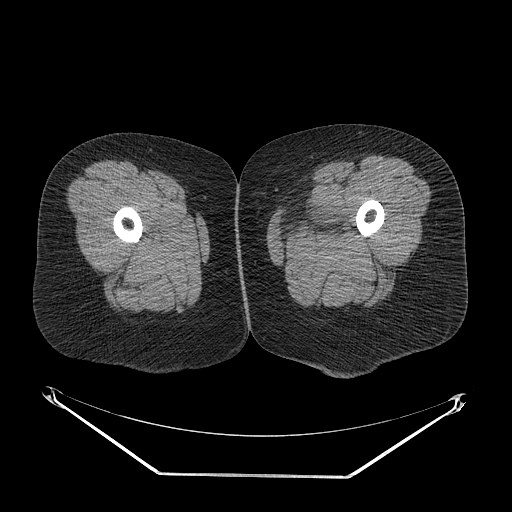
CT of an extremity soft-tissue mass (from a PET/CT study), one axial slice. Position 13 of 267 along the scan axis. Reconstruction kernel STANDARD. Soft-tissue window (W 400 / L 40 HU). 3.75 mm slice thickness. 512 × 512 image matrix, field of view 500 × 500 mm. Female patient. From the clinical record (not read from this slice): histological type: myxofibrosarcoma; grade: intermediate; site of the primary tumour: left thigh.
Structures marked on this image (expert contour drawn on MRI and transferred to this co-registered scan by the dataset authors):
- gross tumour volume including surrounding oedema: box from (x=279, y=201) to (x=353, y=243) px
- gross tumour volume (mass): (x=320, y=203)–(x=334, y=209)